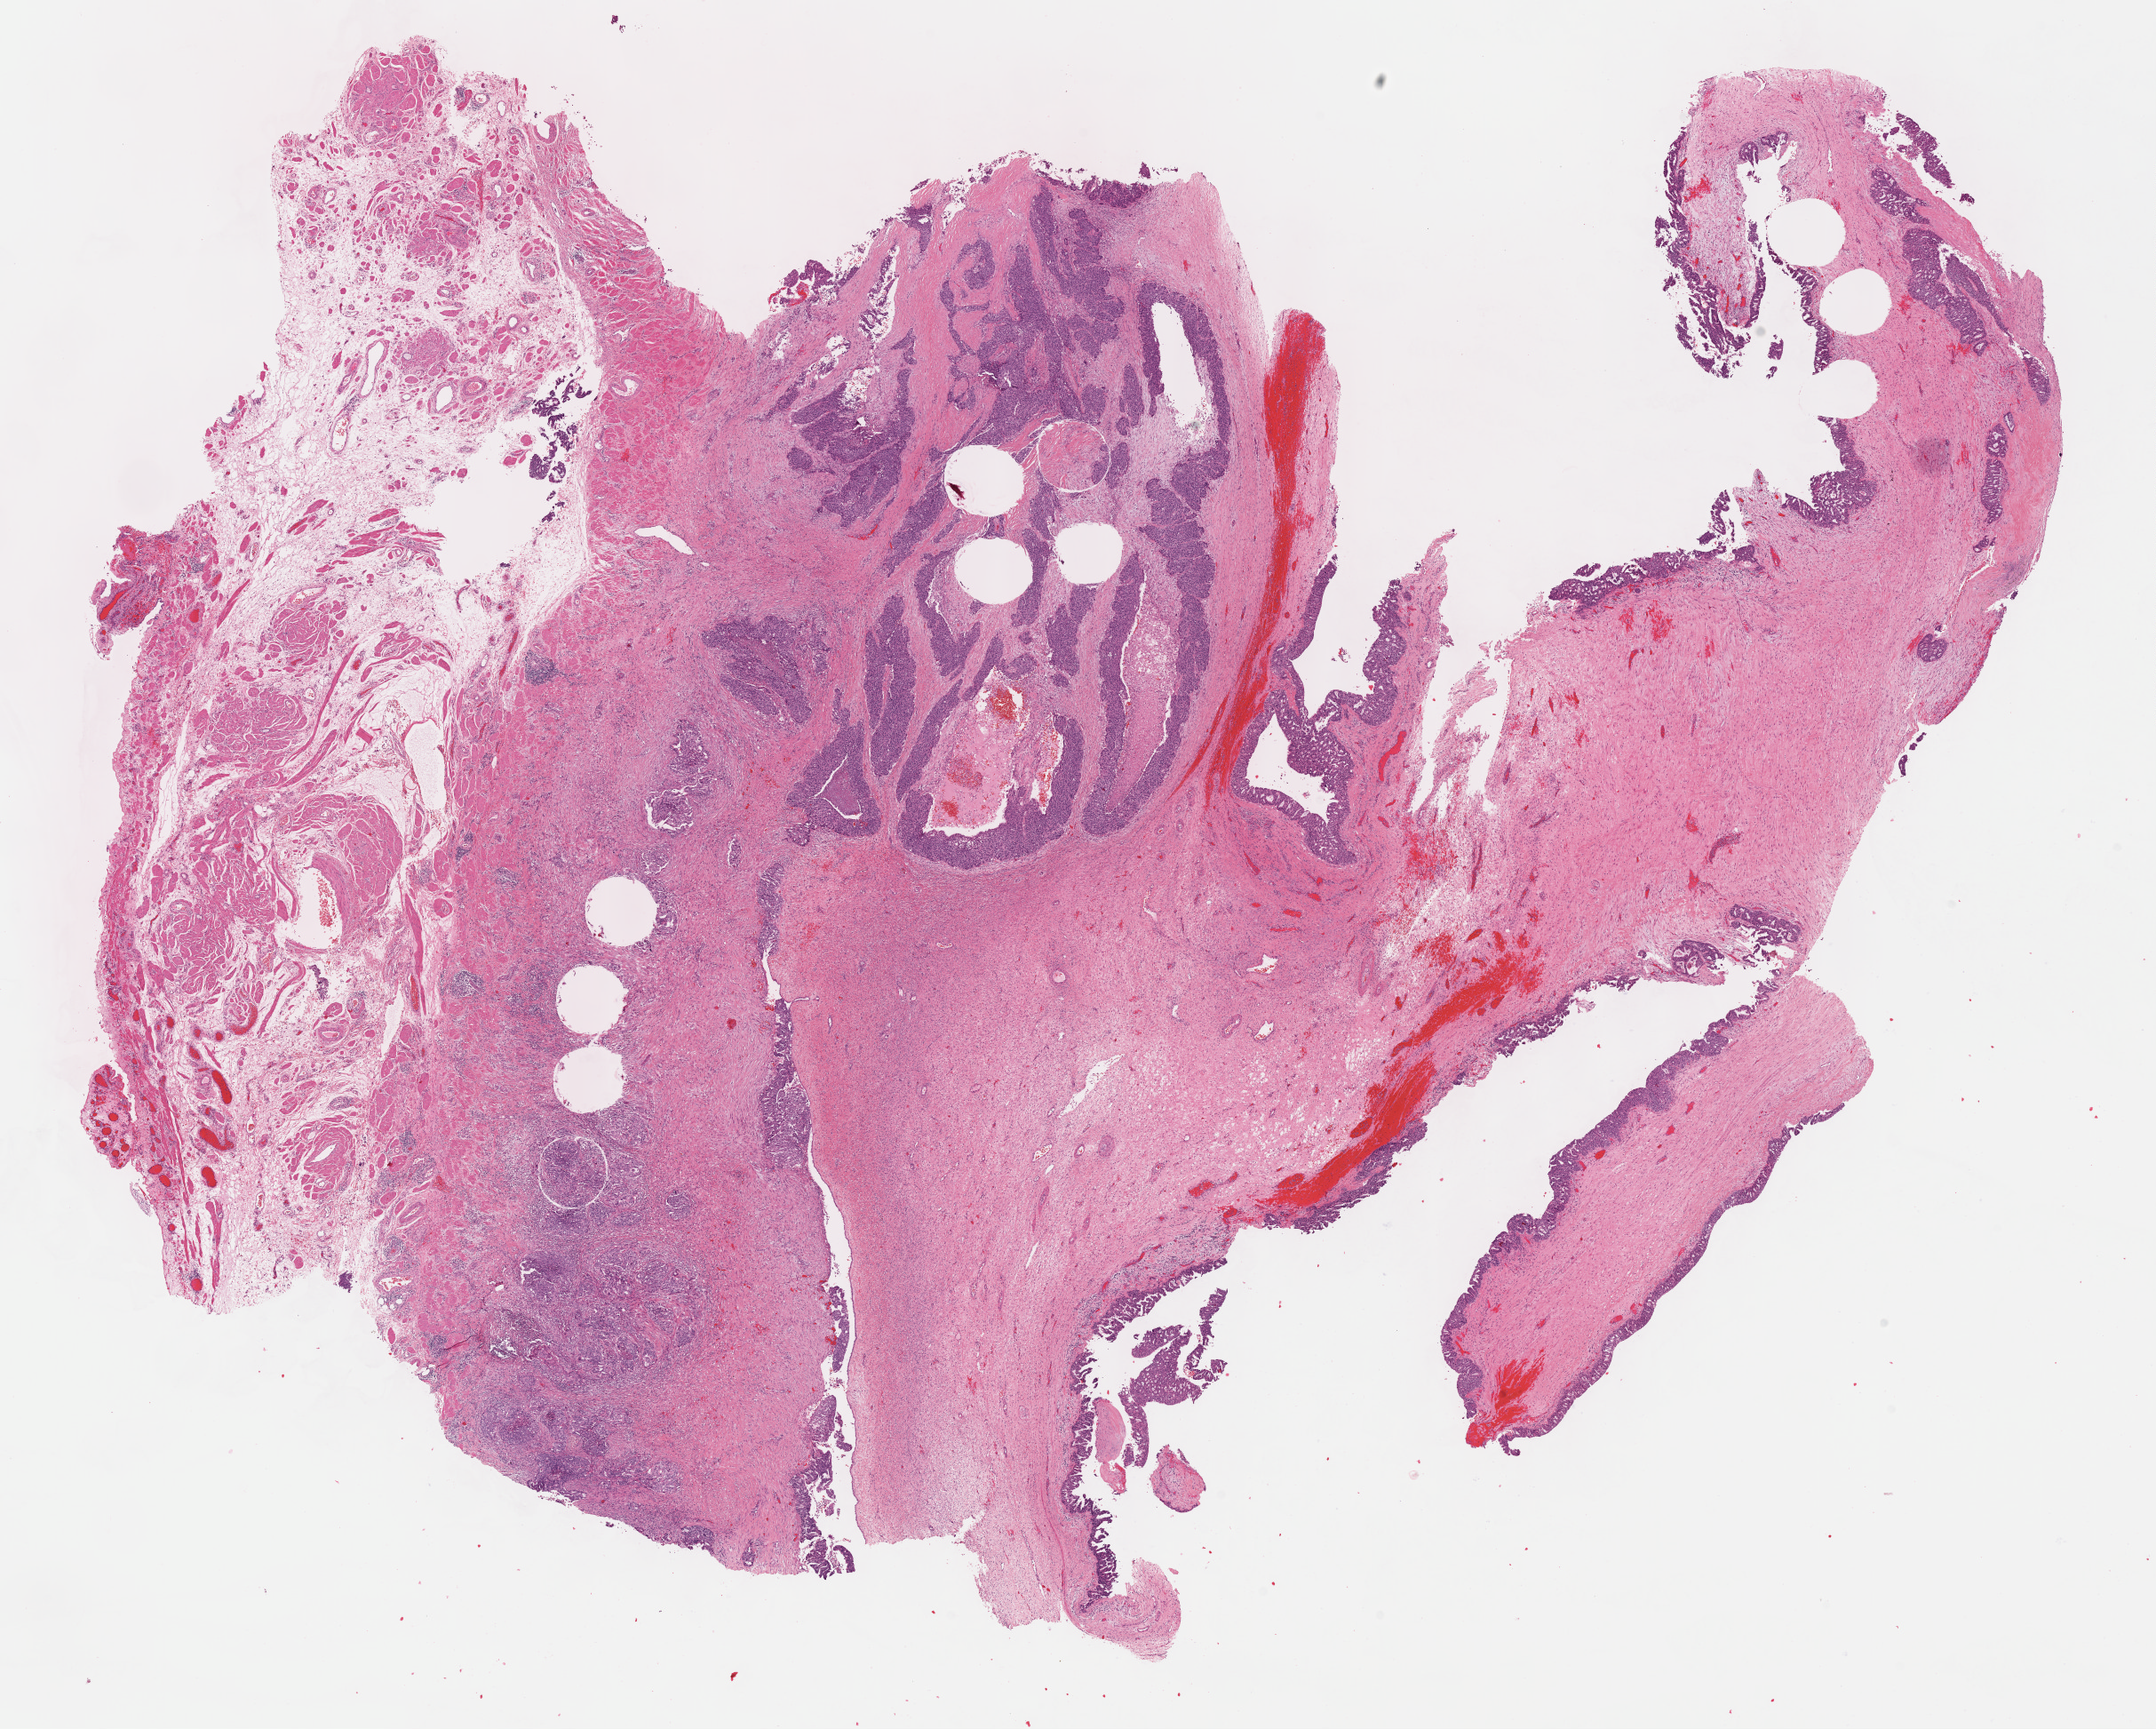
H&E whole-slide image, whole scanned area (about 19.6 x 15.7 mm, slide scanned at 40x) shown as a low-resolution overview. Formalin-fixed paraffin-embedded (FFPE) diagnostic section. Sample: primary tumour, ovary. Female, age 43 years at initial diagnosis. Histologic grade: G3 (poorly differentiated).
FIGO stage: IIIC. Pathologic diagnosis: Serous cystadenocarcinoma, NOS. Laterality: left.